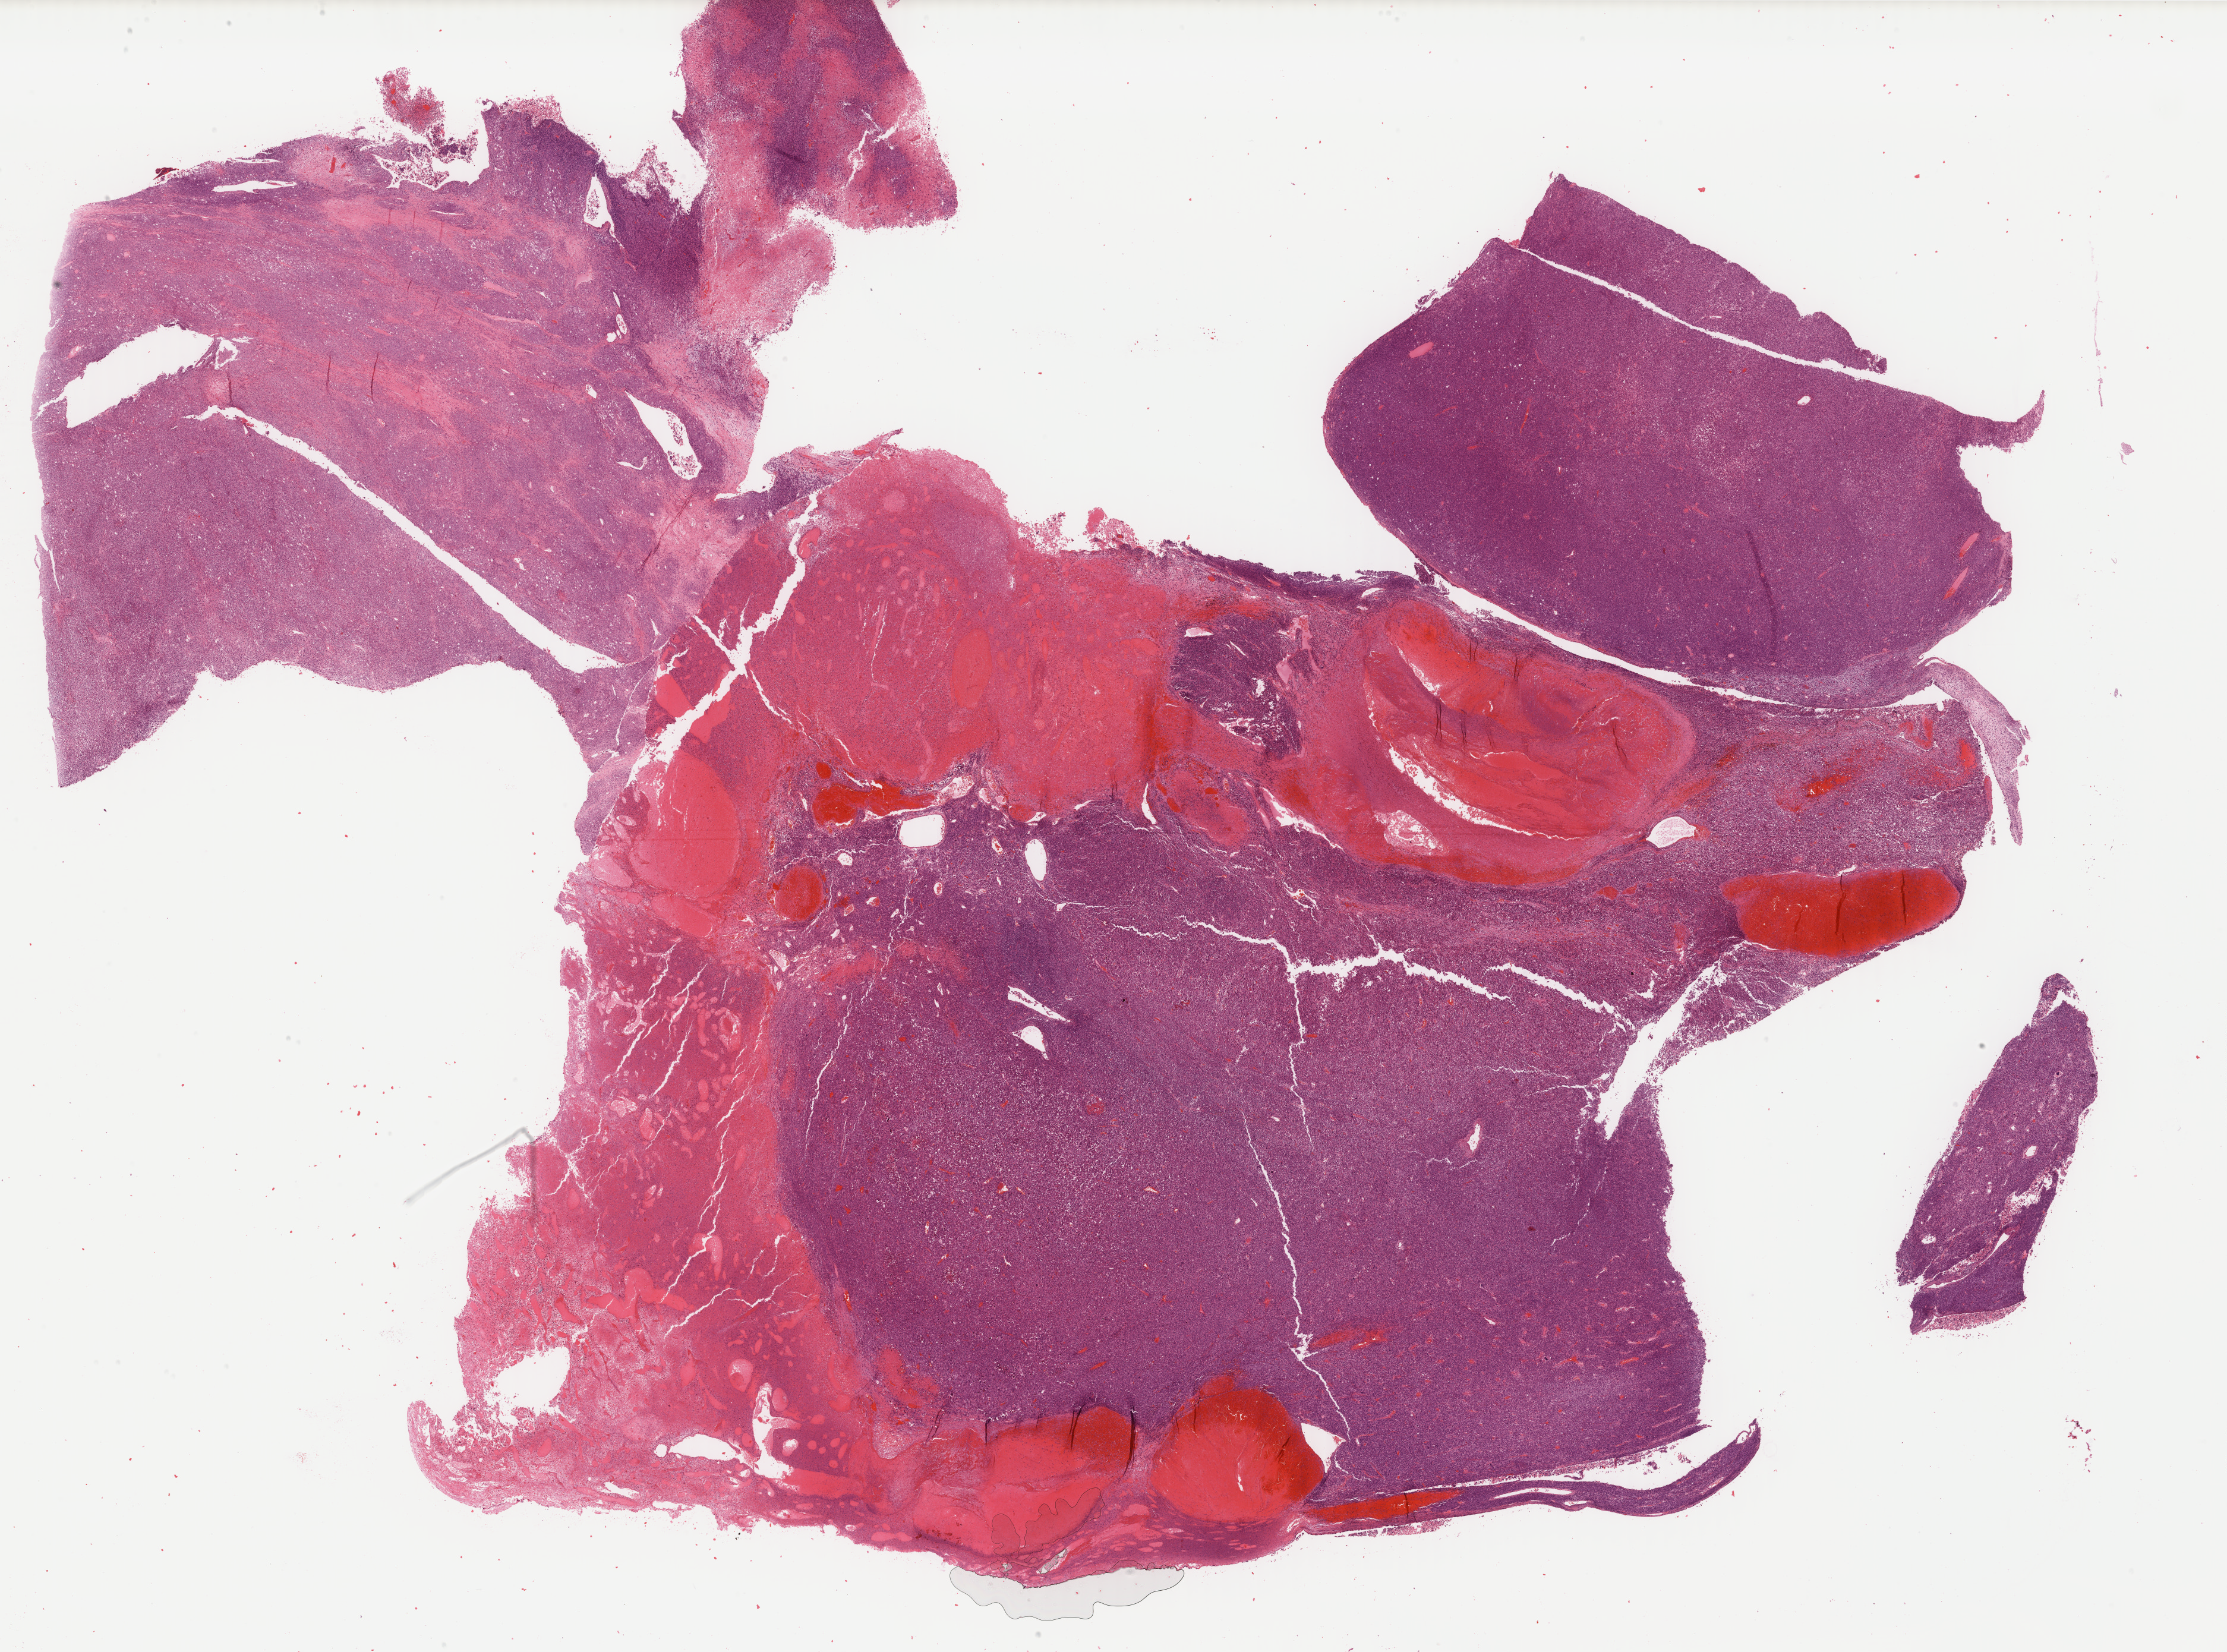
H&E whole-slide image — a low-resolution overview of the entire scanned area, about 29.7 x 22.1 mm (from a 40x scan), formalin-fixed paraffin-embedded (FFPE) diagnostic section, primary tumour sample from the uterus. Female, age 72 years at initial diagnosis.
* FIGO stage: IVB
* histologic diagnosis: Mullerian mixed tumor